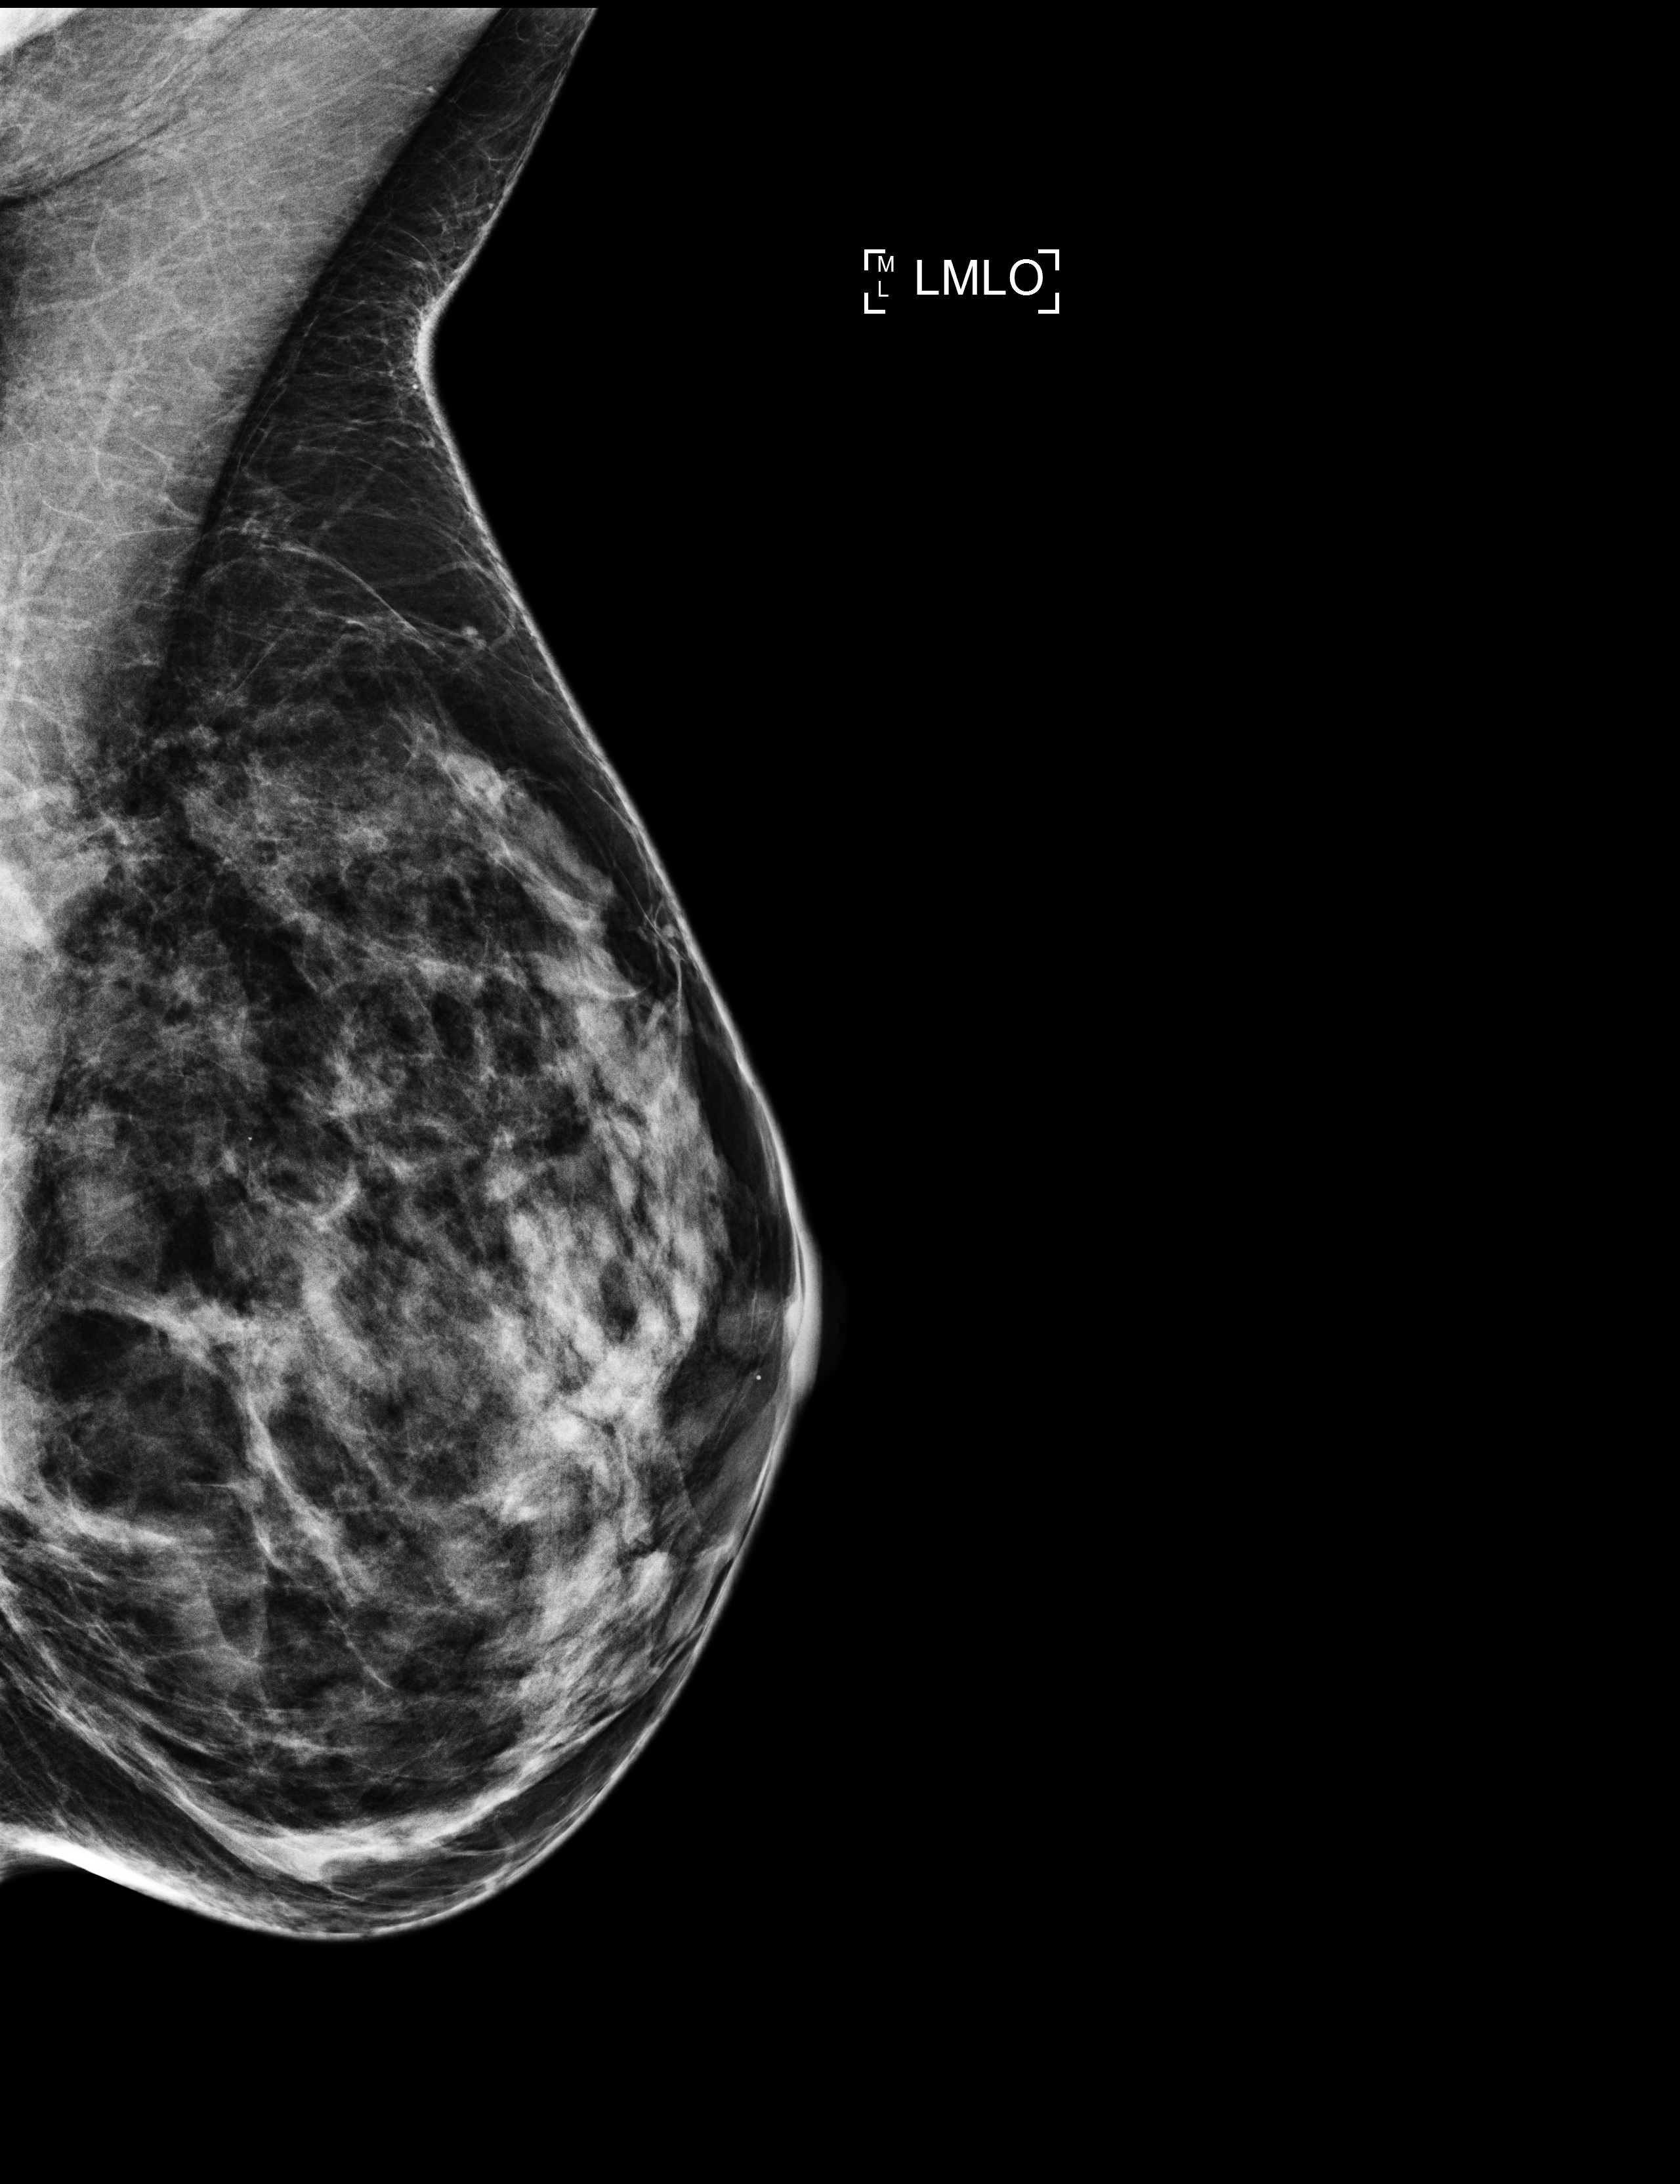
Screening examination. Patient: female, 53 years.
Image type: full-field digital mammogram. Breast: left. Projection: medio-lateral oblique projection.